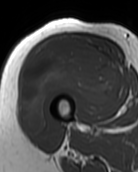
MRI of an extremity soft-tissue mass, one axial slice; slice 43 of 99 in the series (ordered by position); MR volume resampled by the dataset authors to the PET/CT grid (not the native acquisition matrix); 3.27 mm slice thickness; 138 × 172 image matrix, field of view 135 × 168 mm. Female patient. Case-level facts recorded for this patient, not image findings: histological type: pleiomorphic undifferentiated sarcoma; grade: high; site of the primary tumour: right quadricep.
Outlined on this slice (expert contour drawn on MRI and transferred to this co-registered scan by the dataset authors):
- gross tumour volume including surrounding oedema: box from (x=21, y=38) to (x=120, y=133) px
- gross tumour volume (mass): (x=21, y=38)–(x=120, y=133)